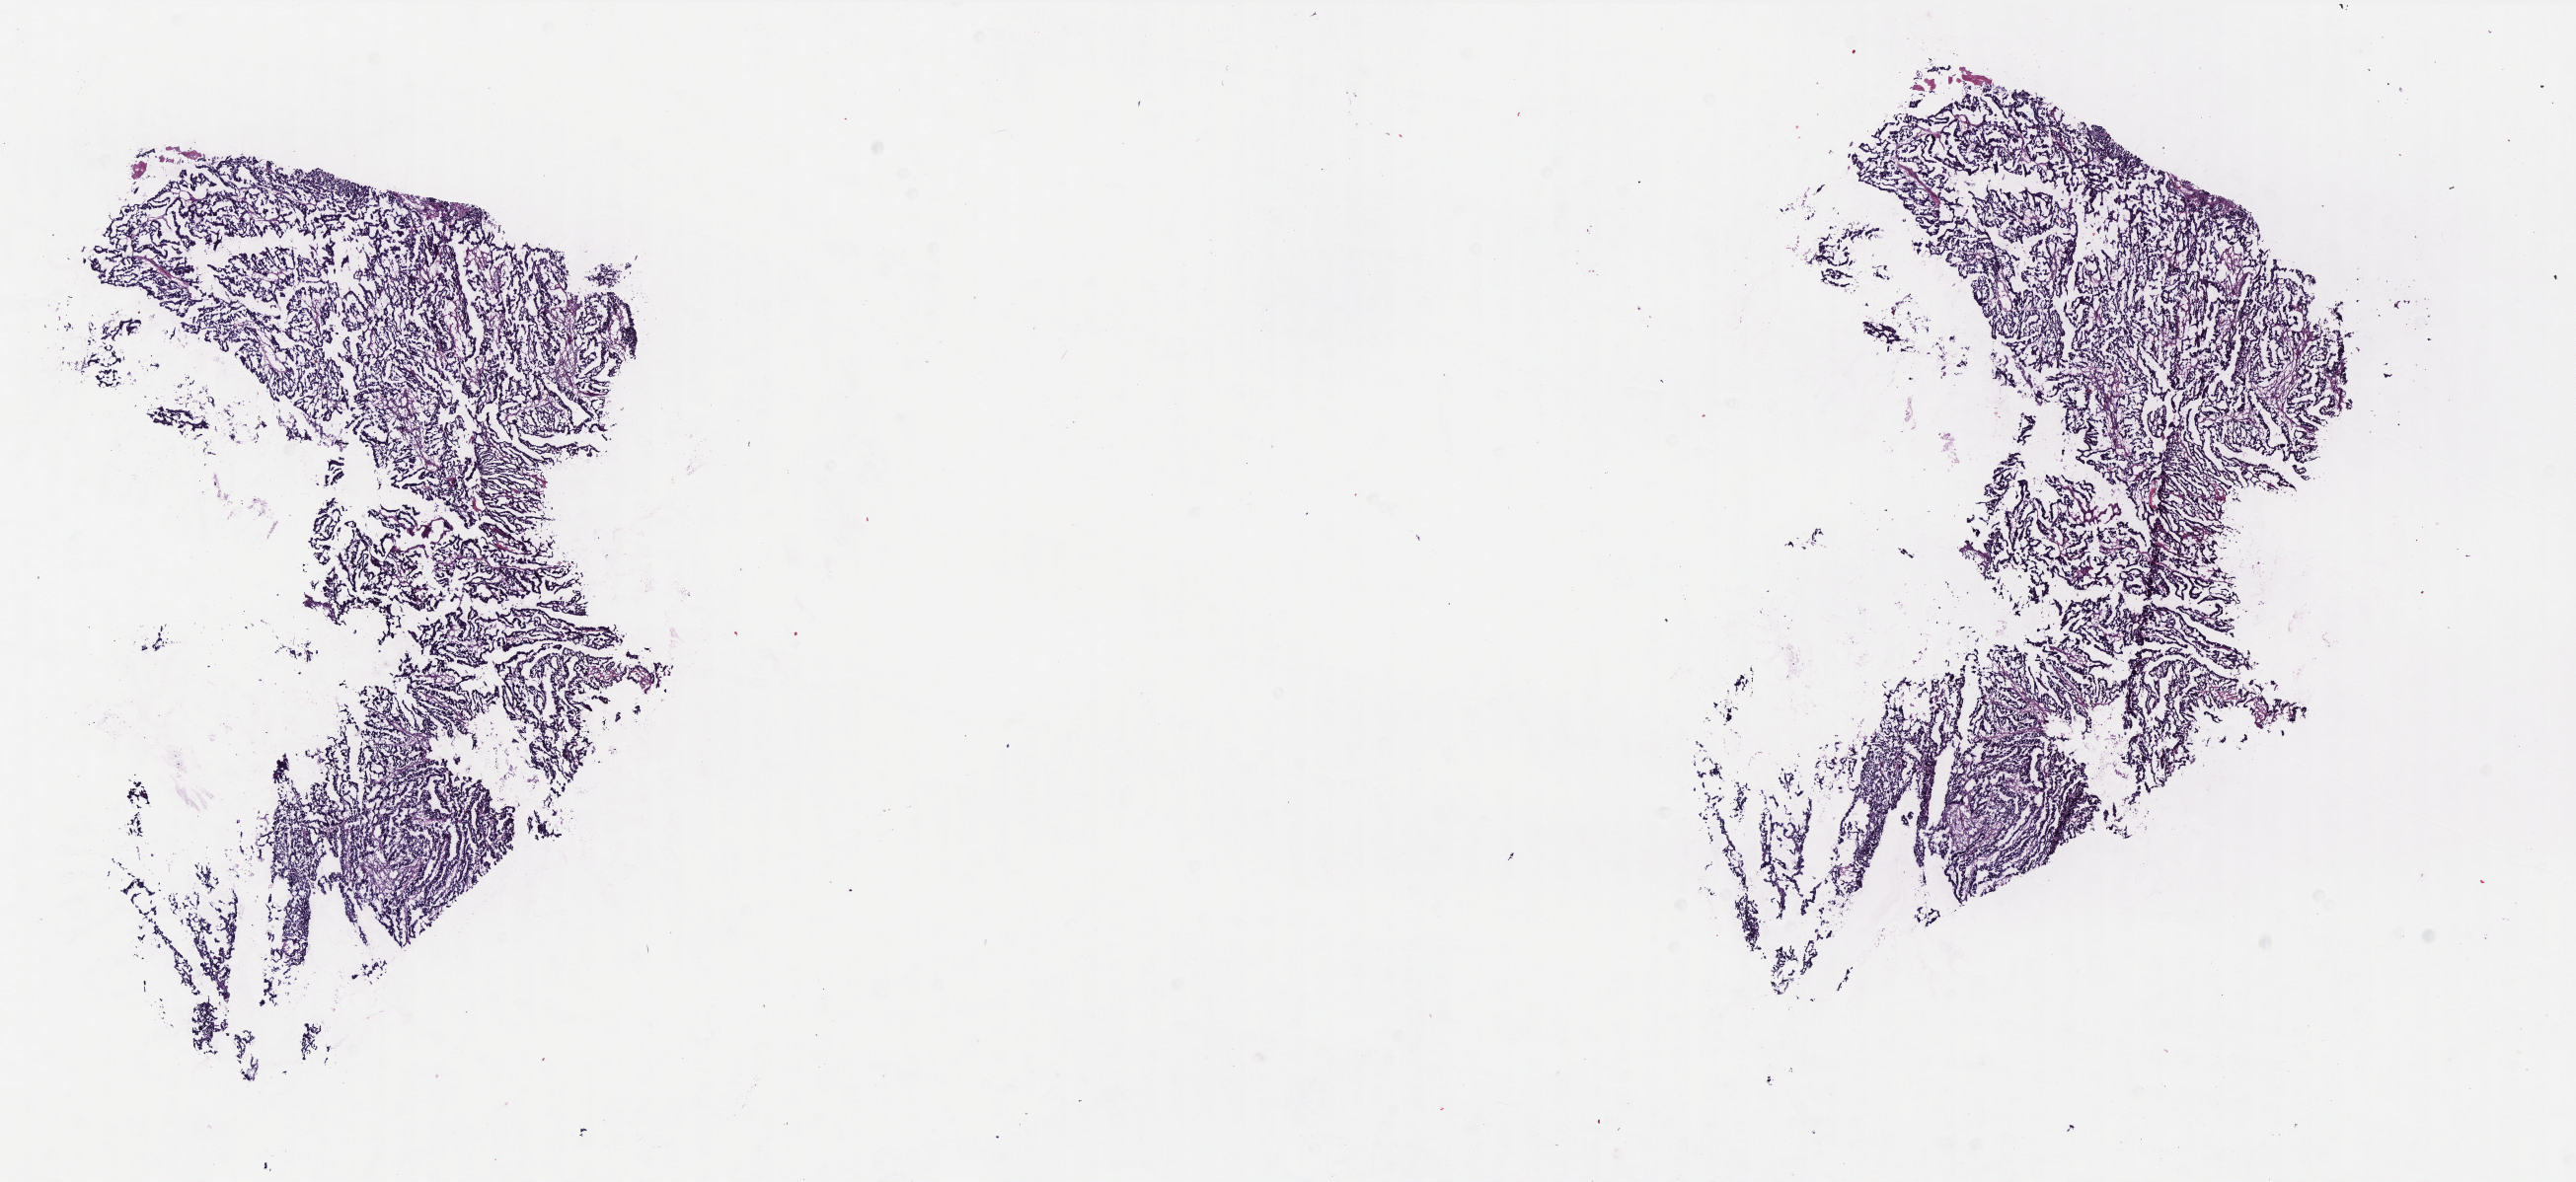
Whole-slide histology image, Hematoxylin and eosin (H&E) stained, whole scanned area (about 20.9 x 9.6 mm) shown as a low-resolution overview, frozen section, sample: primary tumour, uterus. Patient: female, age at initial diagnosis 57 years. Histologic grade: G3 (poorly differentiated). Slide review estimates, as recorded: tumour cells 94%, tumour nuclei 95%, normal cells 0%, stromal cells 5%, necrosis 1%. Infiltration values recorded for this section: lymphocyte infiltration 1%, monocyte infiltration 0%, neutrophil infiltration 0%.
FIGO stage: IA. Lymph nodes positive (case pathology): 0 of 19 examined. Pathologic diagnosis: Endometrioid adenocarcinoma, NOS (endometrium).